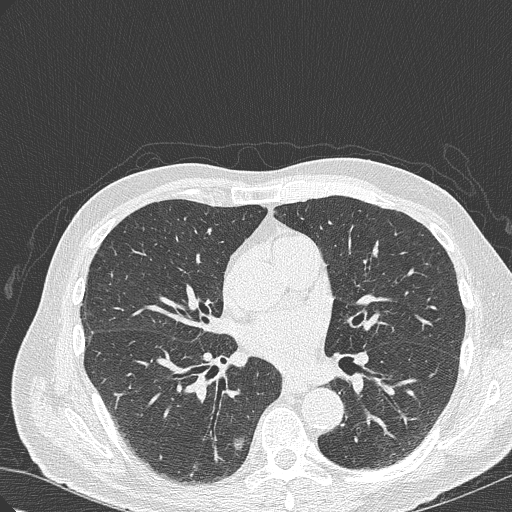
Chest CT (low-dose screening protocol), one axial image. First (baseline) screen. Lung window (W 1500 / L -600 HU). Slice 155 of 322 in the series. 512 × 512 image matrix, field of view 350 × 350 mm. Male, age 70 years at enrolment. Current smoker at enrolment.
Expert-annotated lung lesion, bounding box <196,419,260,484> (left, top, right, bottom; pixels). The screening reader recorded 4 non-calcified nodules or masses ≥4 mm on this exam; which of them this box marks is not recorded. Official screen result: positive, change unspecified: nodule(s) >= 4 mm or enlarging nodule(s), mass(es), or other non-specific abnormalities suspicious for lung cancer. Lung cancer was diagnosed 978 days after this screen (after the third annual screen): bronchiolo-alveolar adenocarcinoma, NOS, right lower lobe, poorly differentiated (G3), stage IB (AJCC 6th edition), 30 mm at pathology.